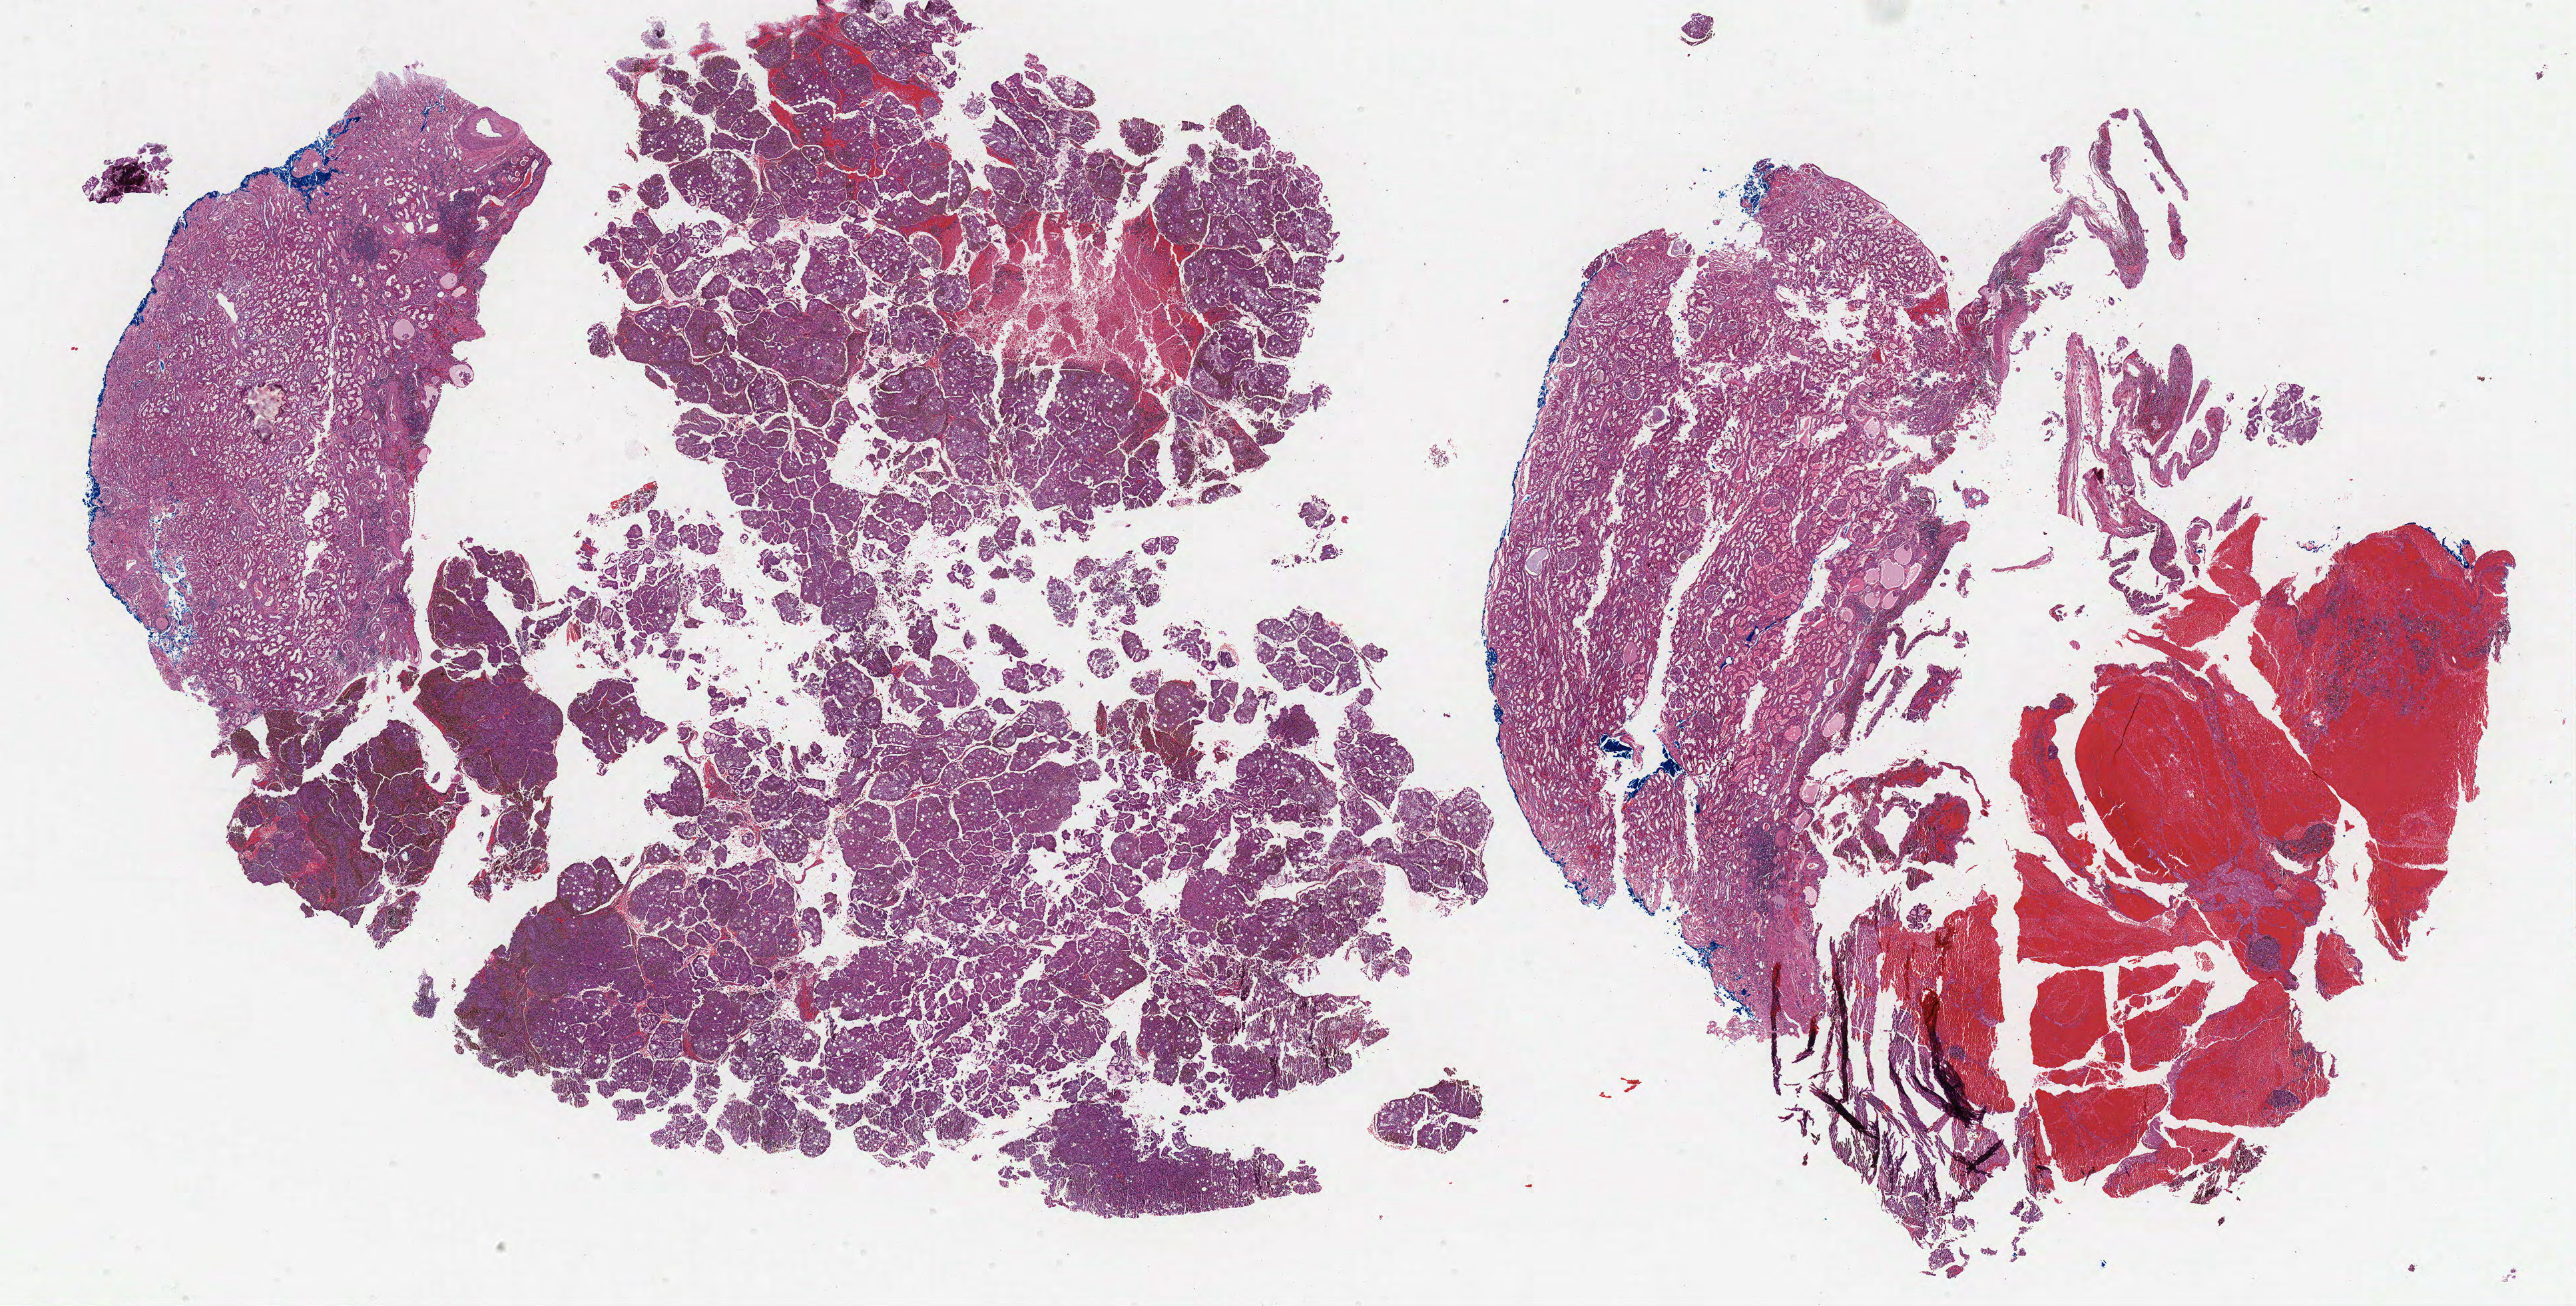
Whole-slide histology image, H&E-stained, shown as a low-resolution overview of the whole scanned area (about 30.9 x 15.7 mm, from a 40x scan), formalin-fixed paraffin-embedded (FFPE) diagnostic section, kidney, primary tumour sample. Male patient; age at initial diagnosis 69 years.
AJCC pathologic stage: I. TNM: T1a NX M0. Diagnosis: Papillary adenocarcinoma, NOS.